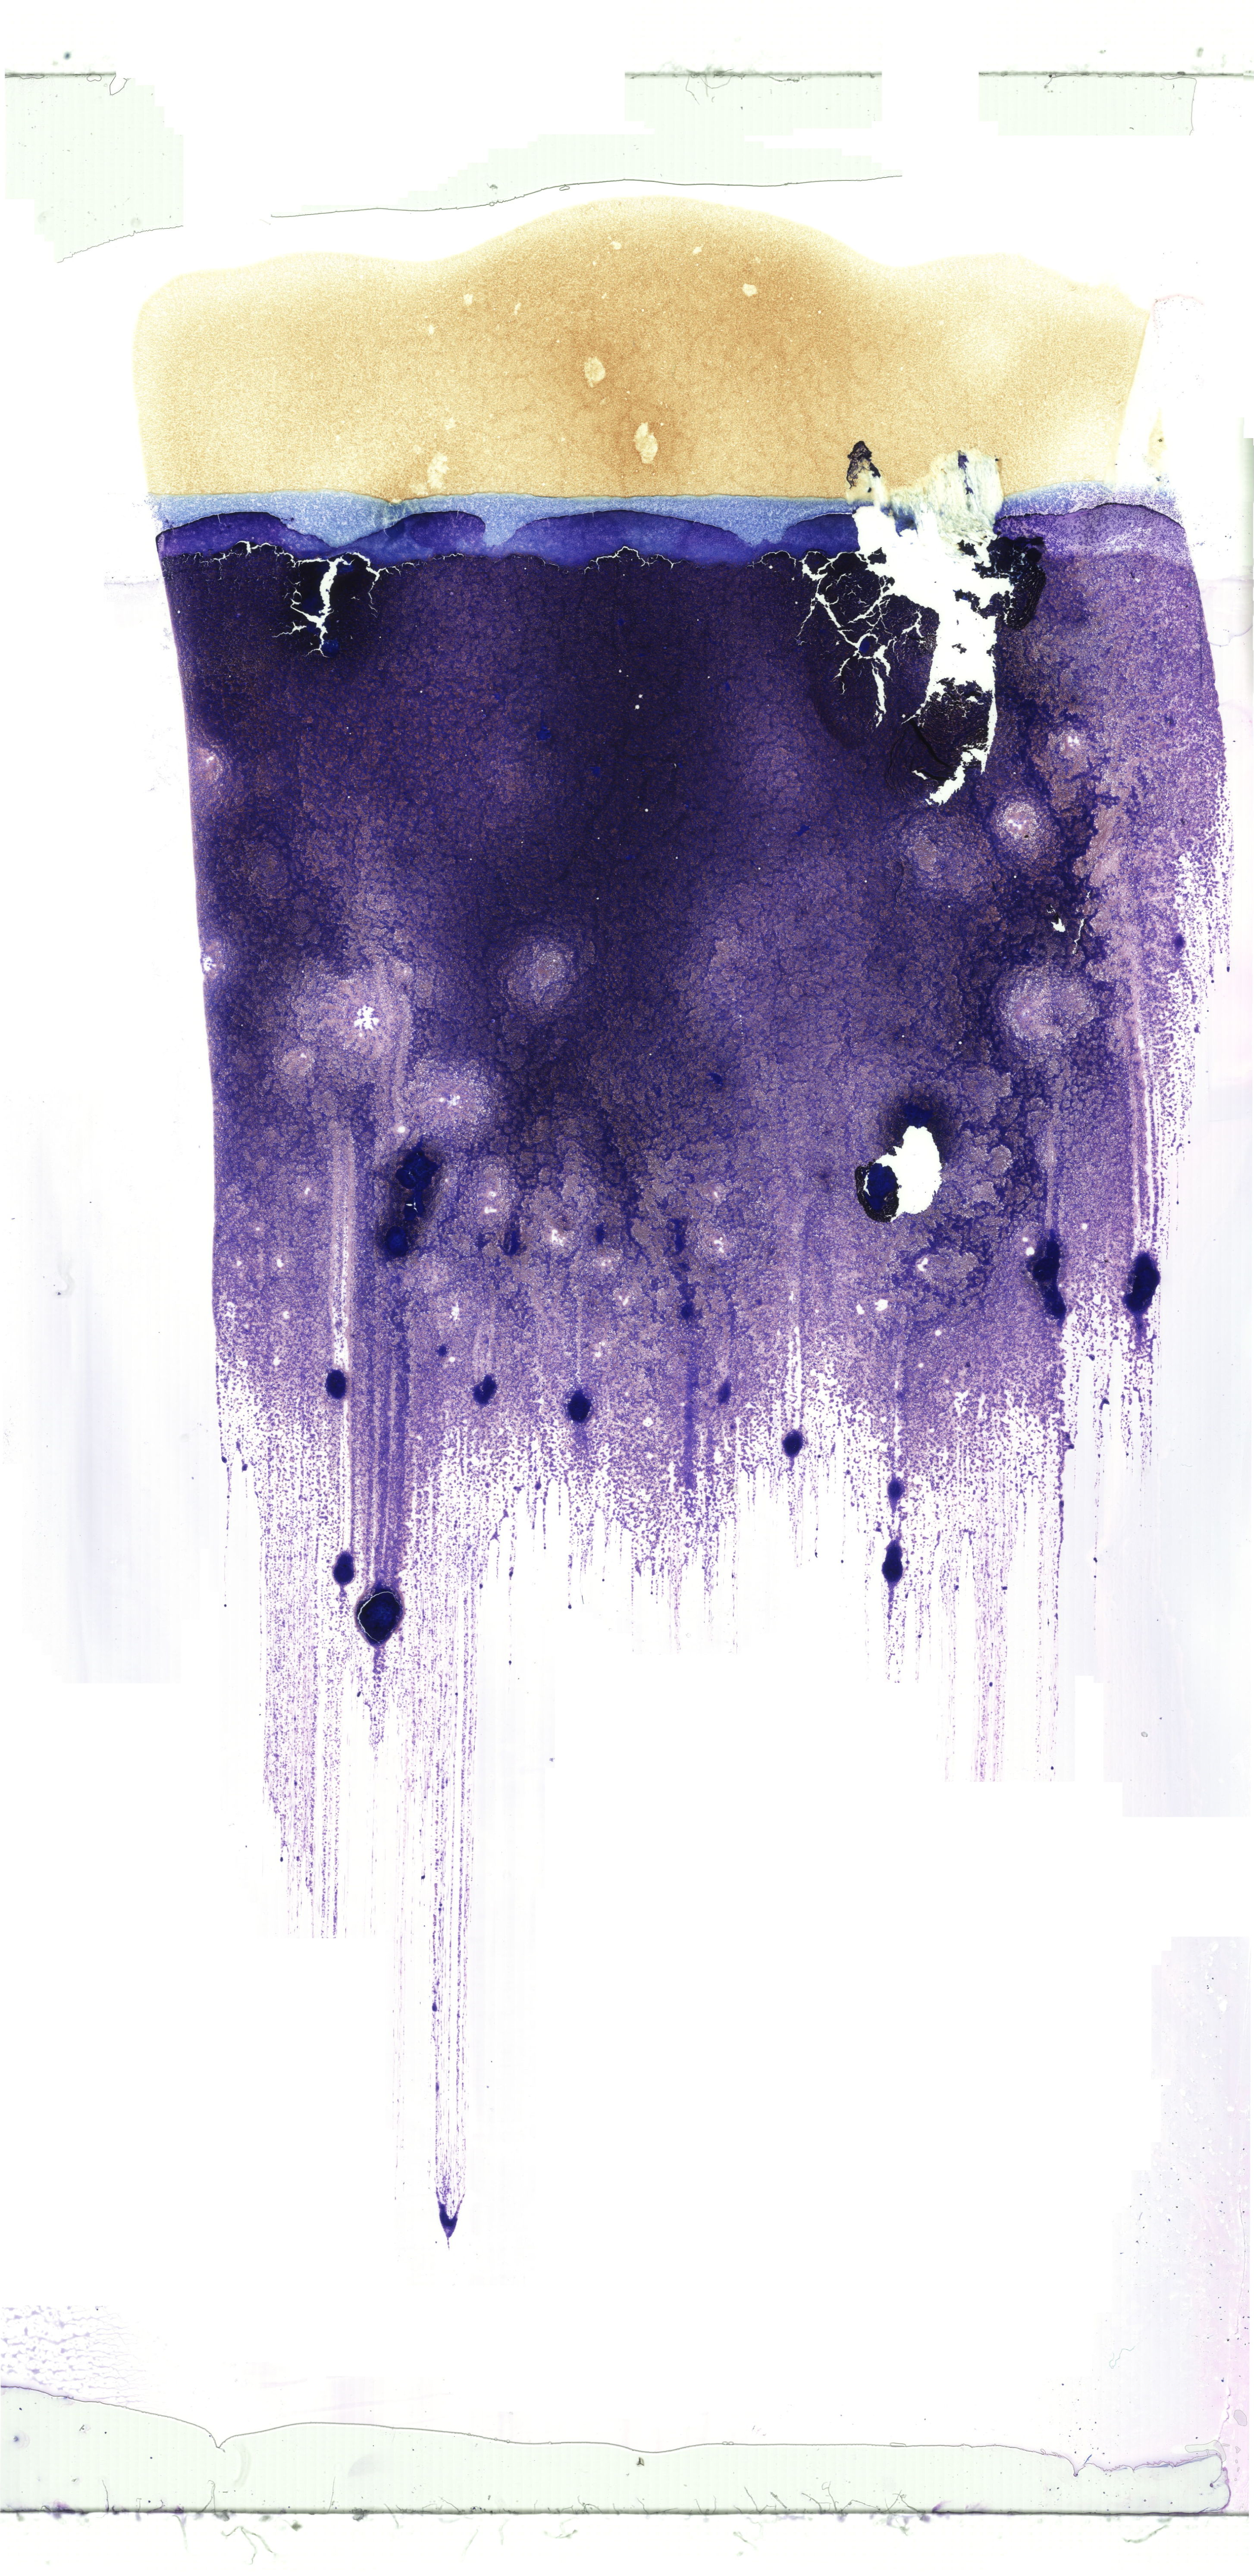
May-Grünwald-Giemsa (MGG)-stained marrow aspirate smear (whole slide), a low-resolution overview of the entire scanned area, about 20.6 x 42.3 mm. Female patient.
Diagnosis: Acute Monocytic Leukemia.